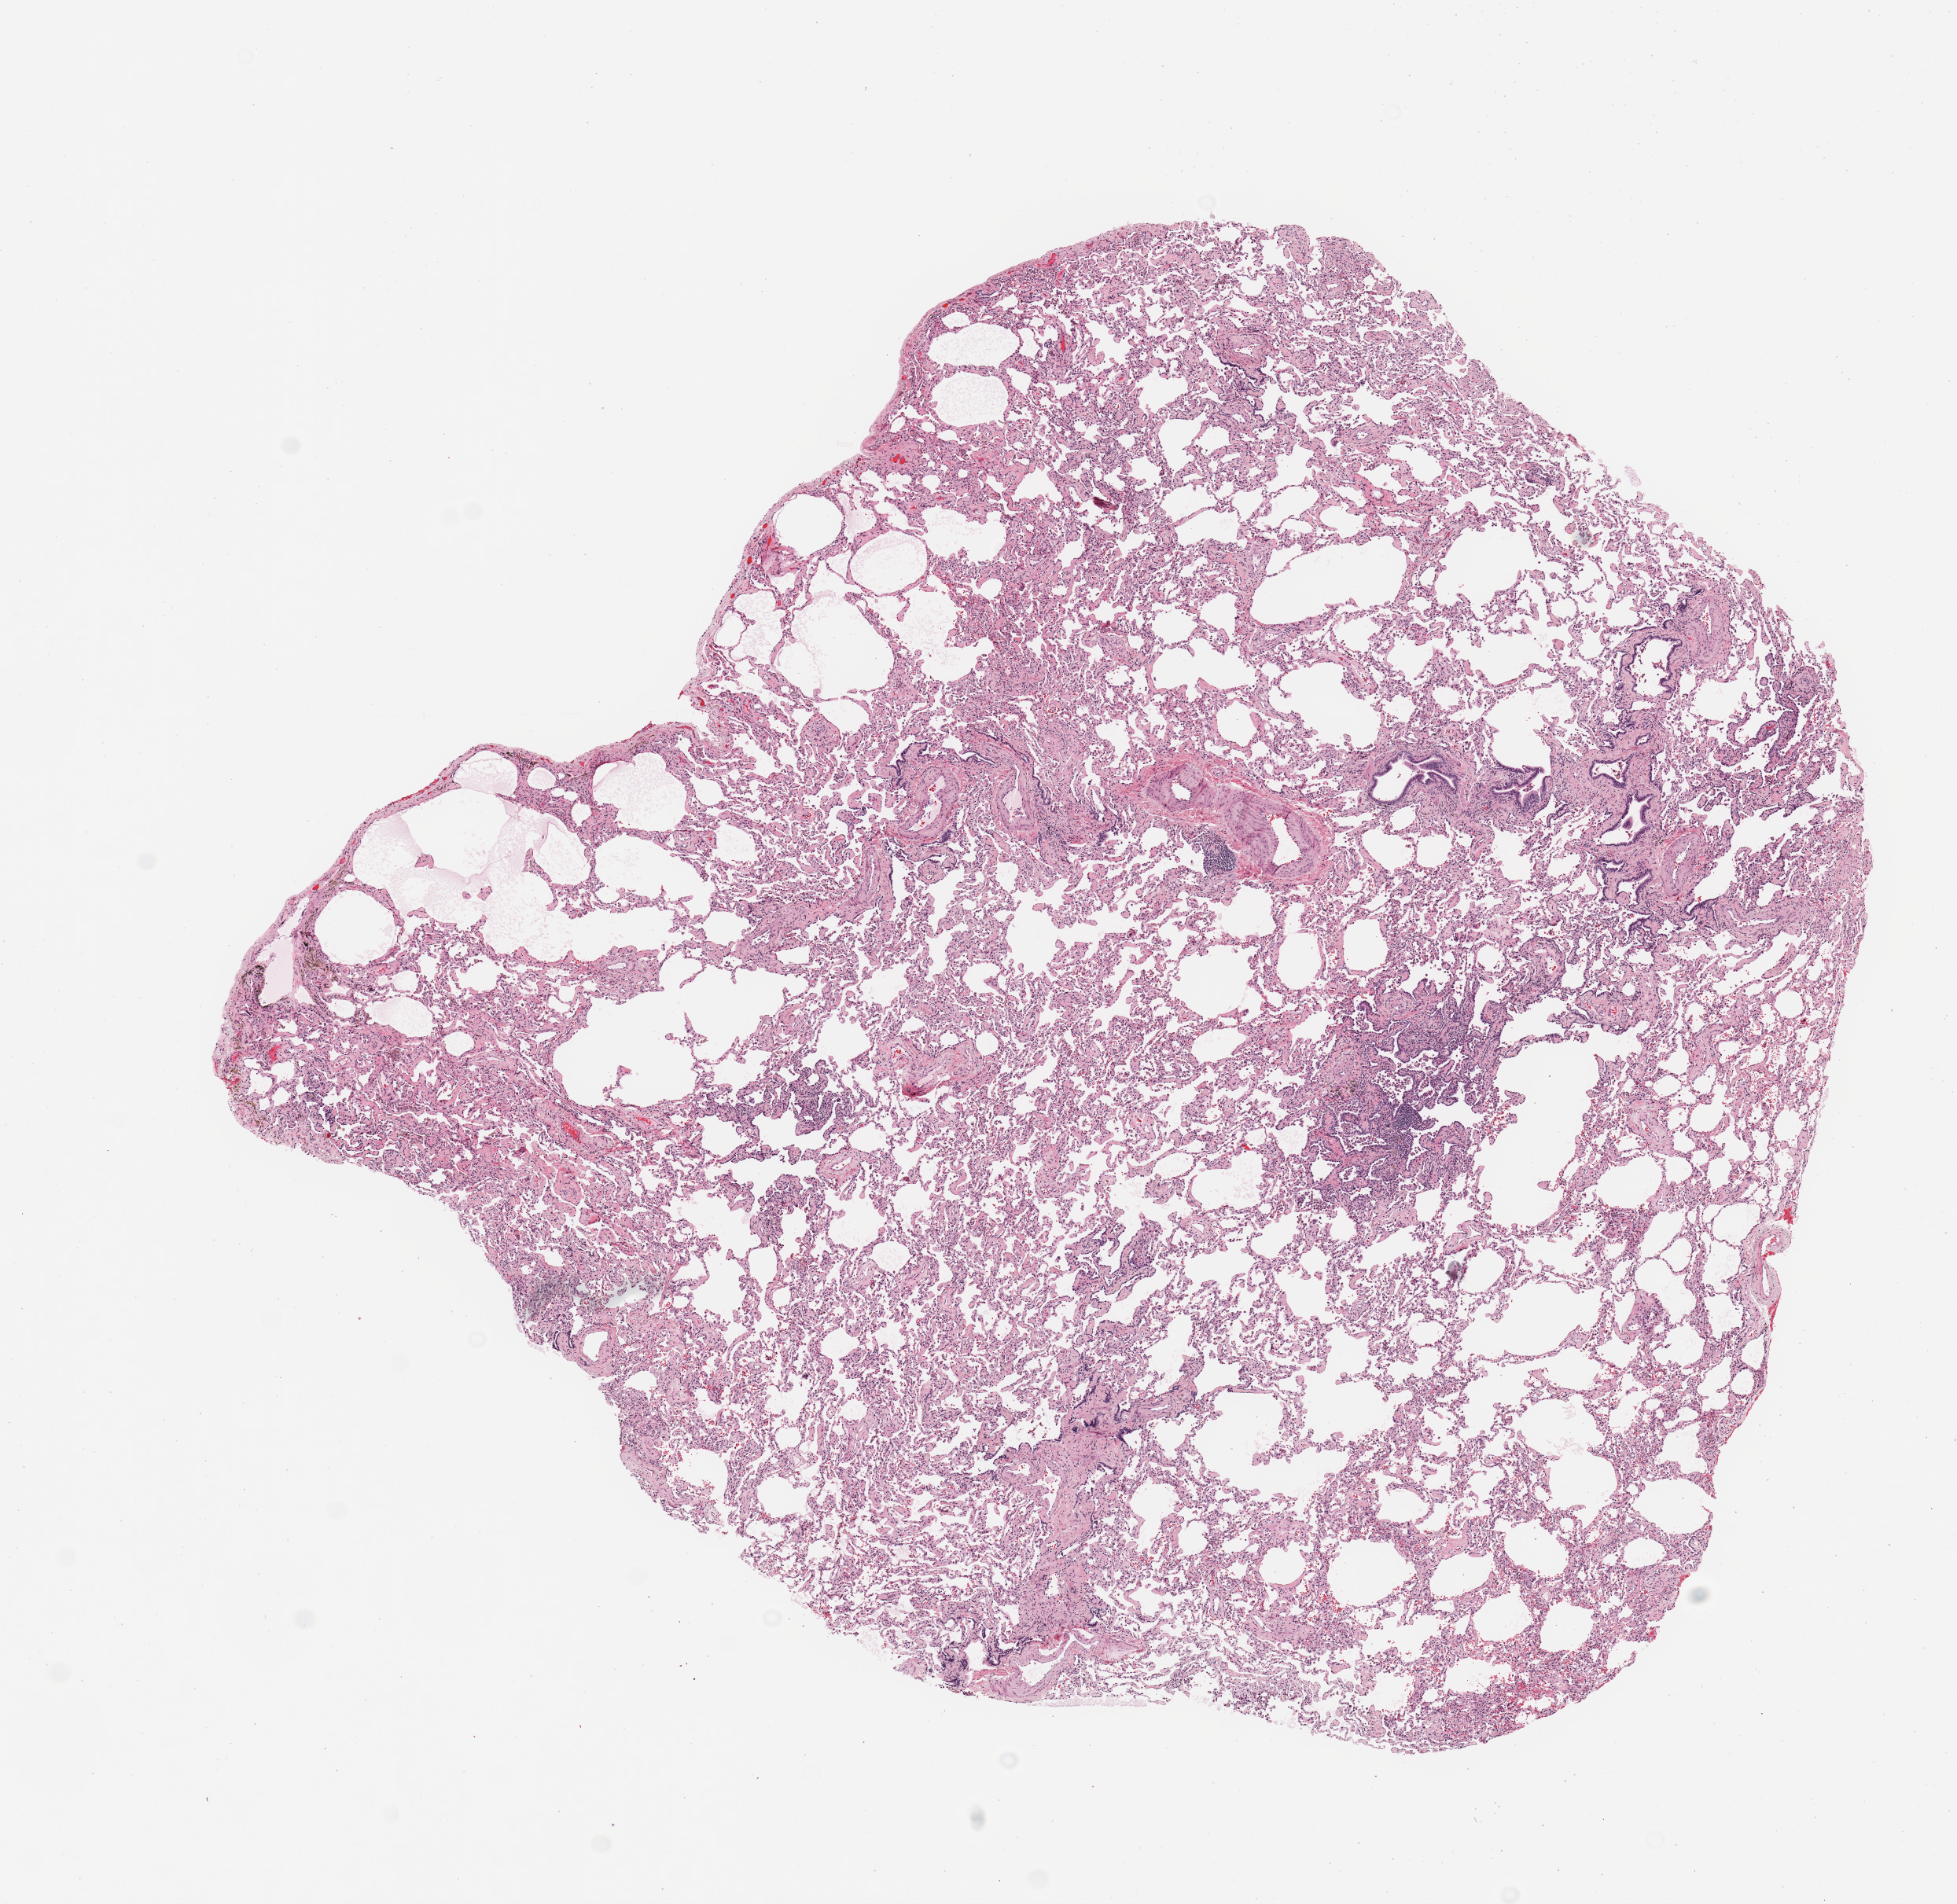
Whole-slide histology image, H&E, whole scanned area (about 9.8 x 9.6 mm, acquisition: 20x scan) shown as a low-resolution overview; normal (non-tumour) tissue sample, sampled site: lung. Female, 61 y/o.
This section: normal (non-tumour) tissue from the same patient. Patient diagnosis: Squamous cell carcinoma, NOS.